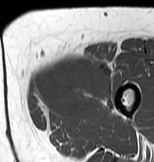
MRI of an extremity soft-tissue mass, one axial slice. Position 20 of 83 along the scan axis. MR volume resampled by the dataset authors to the PET/CT grid (not the native acquisition matrix). 3.27 mm slice thickness. 154 × 162 image matrix, field of view 150 × 158 mm. Female patient. From the clinical record (not read from this slice): histological type: myxofibrosarcoma; grade: intermediate; site of the primary tumour: left thigh.
Outlined on this slice (expert contour drawn on MRI and transferred to this co-registered scan by the dataset authors):
- gross tumour volume including surrounding oedema: bounding box [x1, y1, x2, y2] px = [31, 54, 113, 122]
- gross tumour volume (mass): [35, 57, 111, 122]